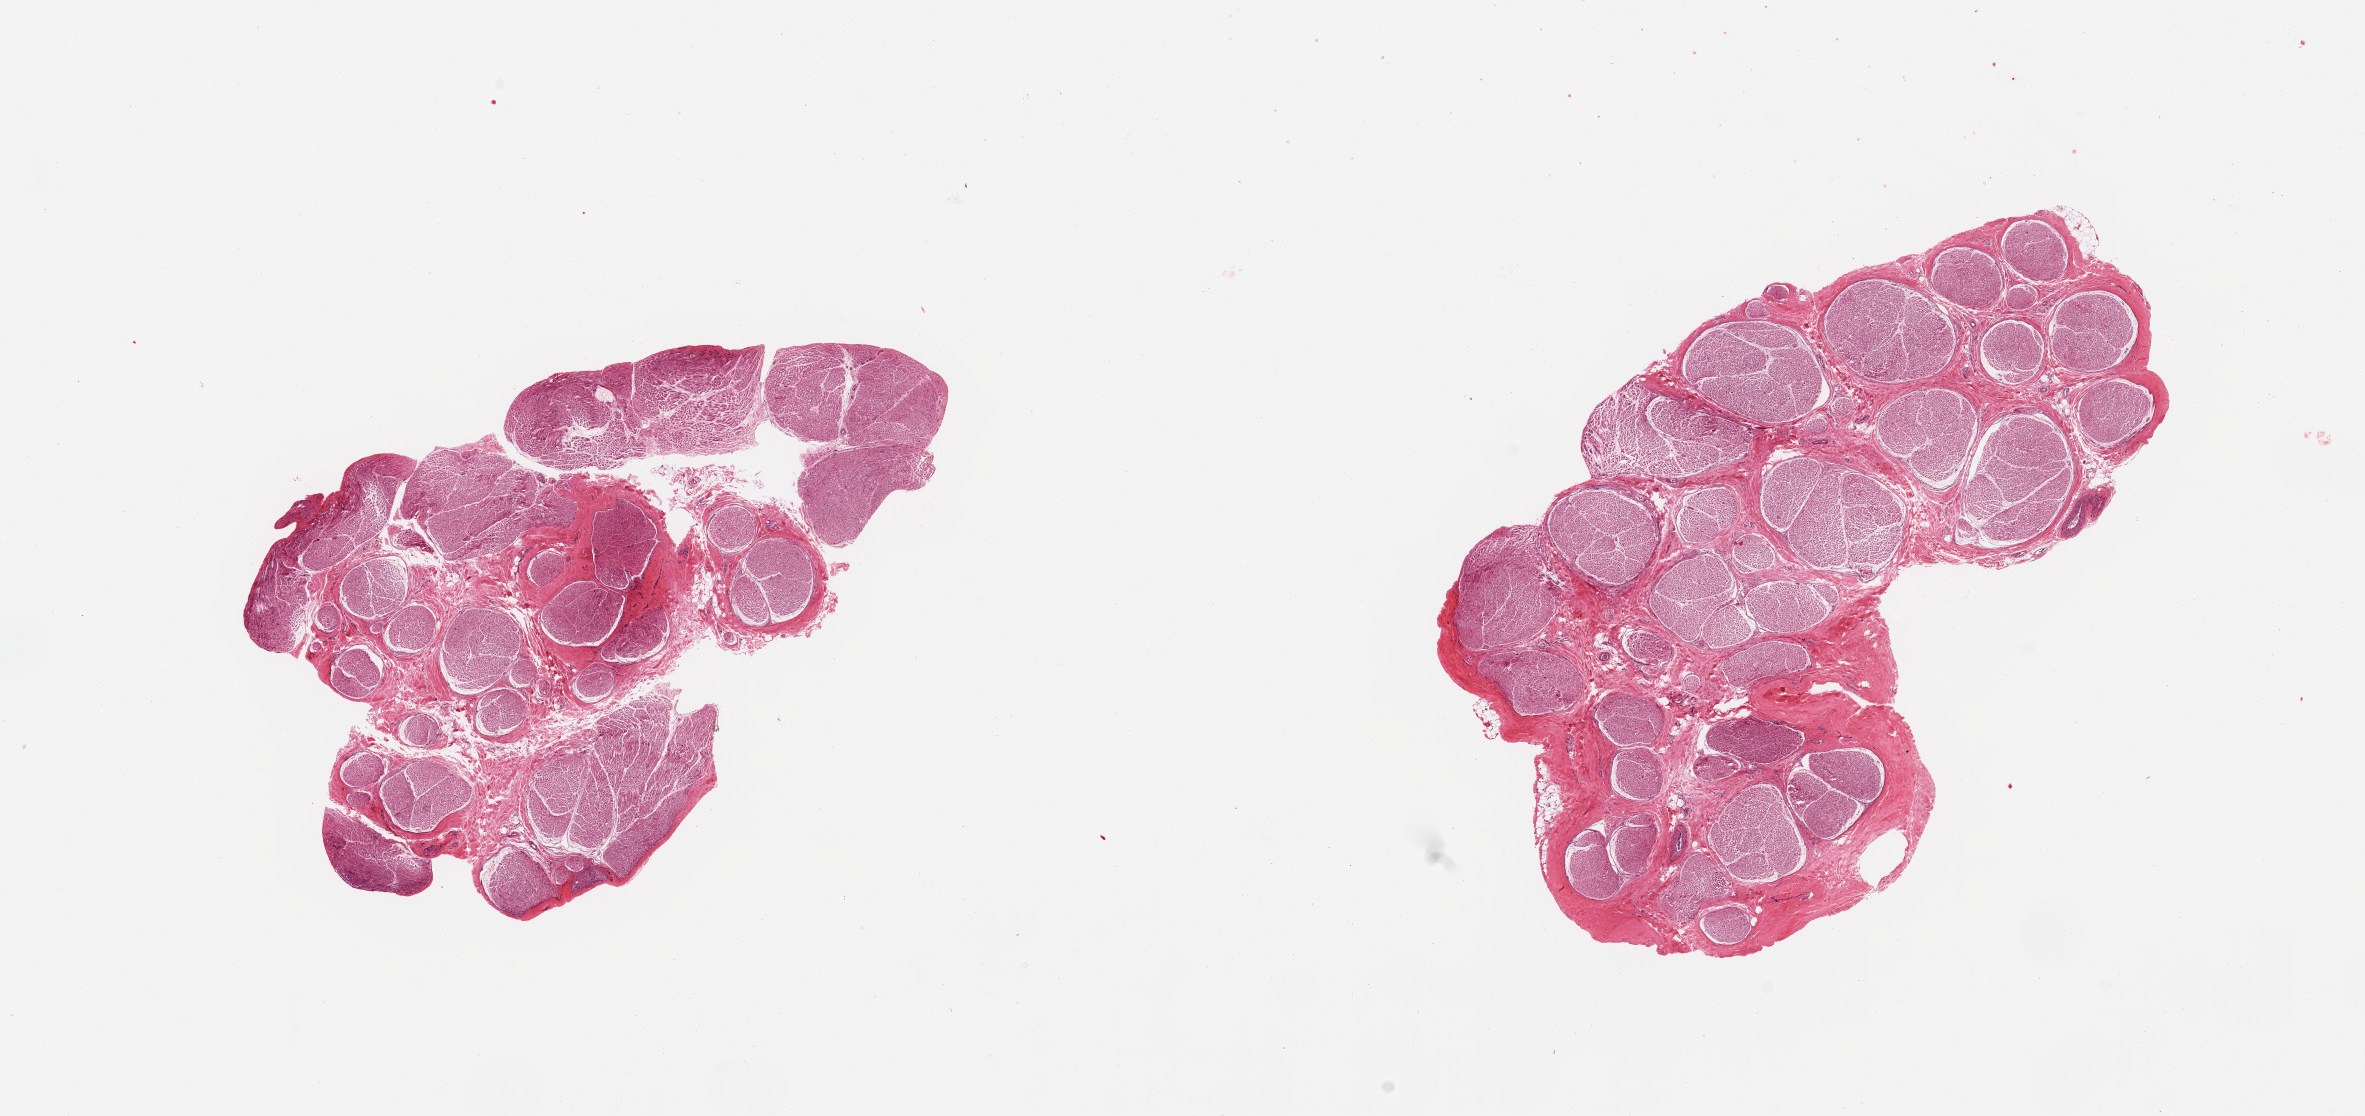
Whole-slide image, haematoxylin and eosin stain — low-resolution overview of the scanned area, about 18.7 x 8.8 mm (slide scanned at 20x), PAXgene-fixed paraffin-embedded (PFPE) section, section of tibial nerve (target tissue), tissue donor sample. Donor: male.
Pathologist's review note for this sample: 2 pieces, no adherent fat; good specimen.